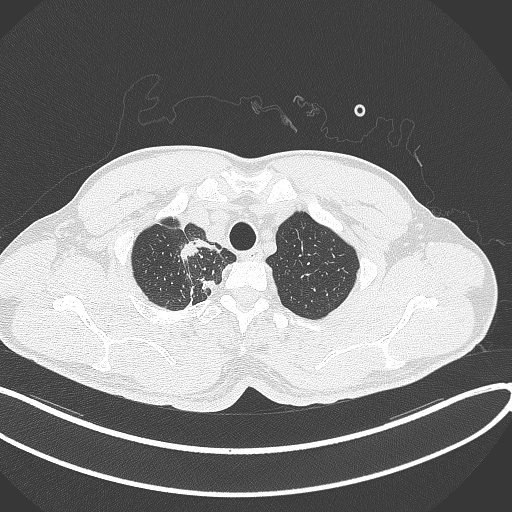
Chest CT, one axial slice. Position 334 of 391 along the scan axis. 120 kVp. Lung window (W 1500 / L -600 HU). 1 mm slice thickness. 512 × 512 image matrix, field of view 400 × 400 mm. Patient: male, 48 years. Case-level facts recorded for this patient, not image findings: clinical TNM (as recorded): T1c N1 M1.
Outlined on this slice (rectangle marked by the reading radiologist):
- lung tumour (recorded histology: adenocarcinoma): bounding box [x1, y1, x2, y2] px = [176, 234, 201, 263]